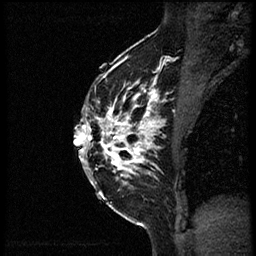
Breast MRI (dynamic contrast-enhanced), one sagittal slice; slice 37 of 56 in the series (ordered by position); dynamic contrast-enhanced study with each time point stored as its own series, time point 2 of 3 at this slice position (early post-contrast, ordered by acquisition time); 1.5 T; TE 4.2 ms, TR 21.3 ms; 2 mm slice thickness; 256 × 256 image matrix, field of view 200 × 200 mm. Patient: female, 41 years. From the clinical record (not read from this slice): setting: breast cancer imaged before/during neoadjuvant chemotherapy; receptor status: HER2-positive.
Outlined on this slice (semi-automatically segmented with operator editing):
- analysis volume of interest (the breast-tissue region the enhancement analysis was run in; not a lesion): bounding box <84,73,177,205> (left, top, right, bottom; pixels)
- tumour enhancement mask (voxels above the 100 % enhancement threshold inside the analysis volume of interest): <84,74,165,183>